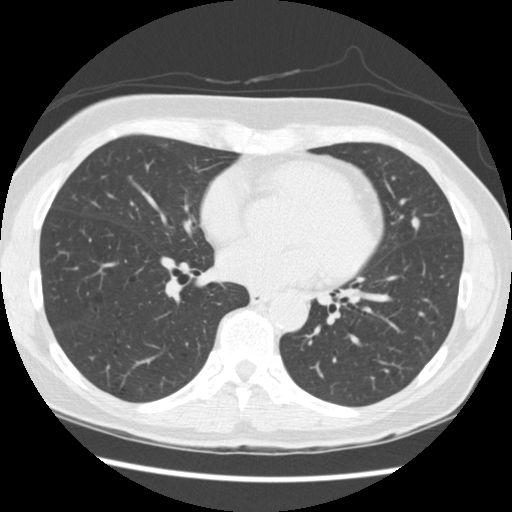
Low-dose screening chest CT, one axial slice; slice 123 of 262 in the series (ordered by position); reconstruction kernel STANDARD; 120 kVp; lung window (W 1500 / L -600 HU); 2.5 mm slice thickness; 512 × 512 image matrix, field of view 340 × 340 mm.
Annotated regions visible in this slice (outlined manually by an expert reader):
- lesion 2 (tumor, lingular bronchus): bounding box [x1, y1, x2, y2] px = [412, 218, 419, 228]